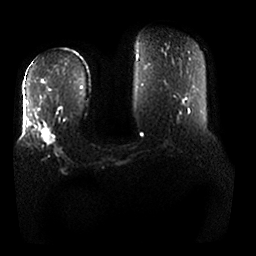
Breast MRI, one axial slice; slice 8 of 25 in the series (ordered by position); diffusion-weighted series; image 2 of 4 stored at this slice position (different b-values; order by instance number); 1.5 T; 4 mm slice thickness; 256 × 256 image matrix, field of view 380 × 380 mm. Female patient.
Outlined on this slice (expert manual segmentation):
- tumour on diffusion-weighted imaging: bounding box [x1, y1, x2, y2] px = [41, 125, 55, 147]